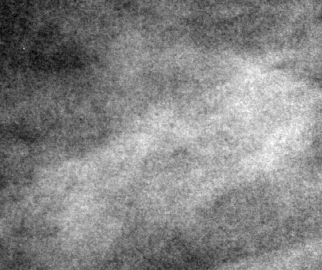
Crop from a digitized film mammogram around one marked abnormality, right breast, MLO view.
Mass, shape lobulated / irregular, margins microlobulated / ill defined; BI-RADS assessment category 4; pathology result (as recorded, not read from the image): benign.